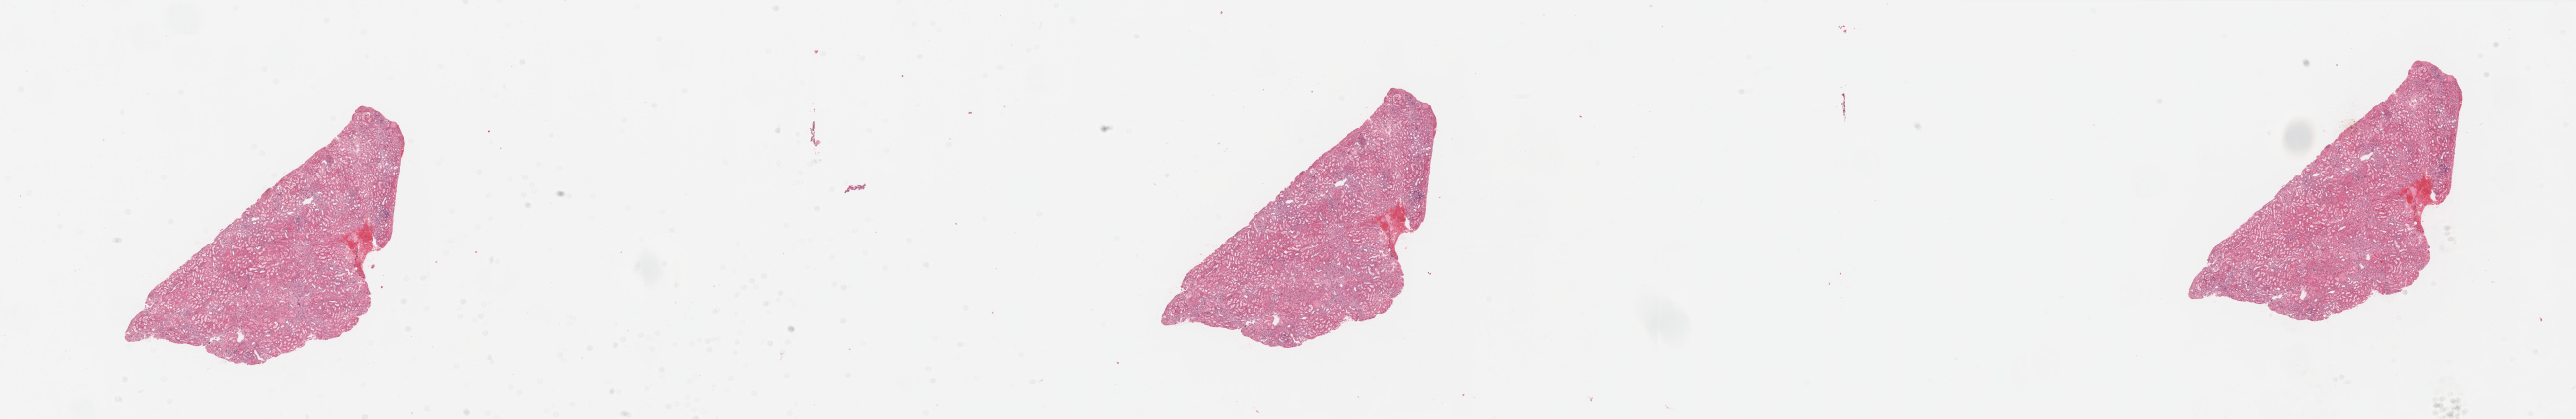
Digitized H&E tissue section (whole slide), low-resolution overview of the scanned area, about 41.3 x 6.7 mm. Normal (non-tumour) tissue sample, kidney. 51-year-old female patient.
* this section: normal (non-tumour) tissue from the same patient
* patient diagnosis: Renal cell carcinoma, NOS